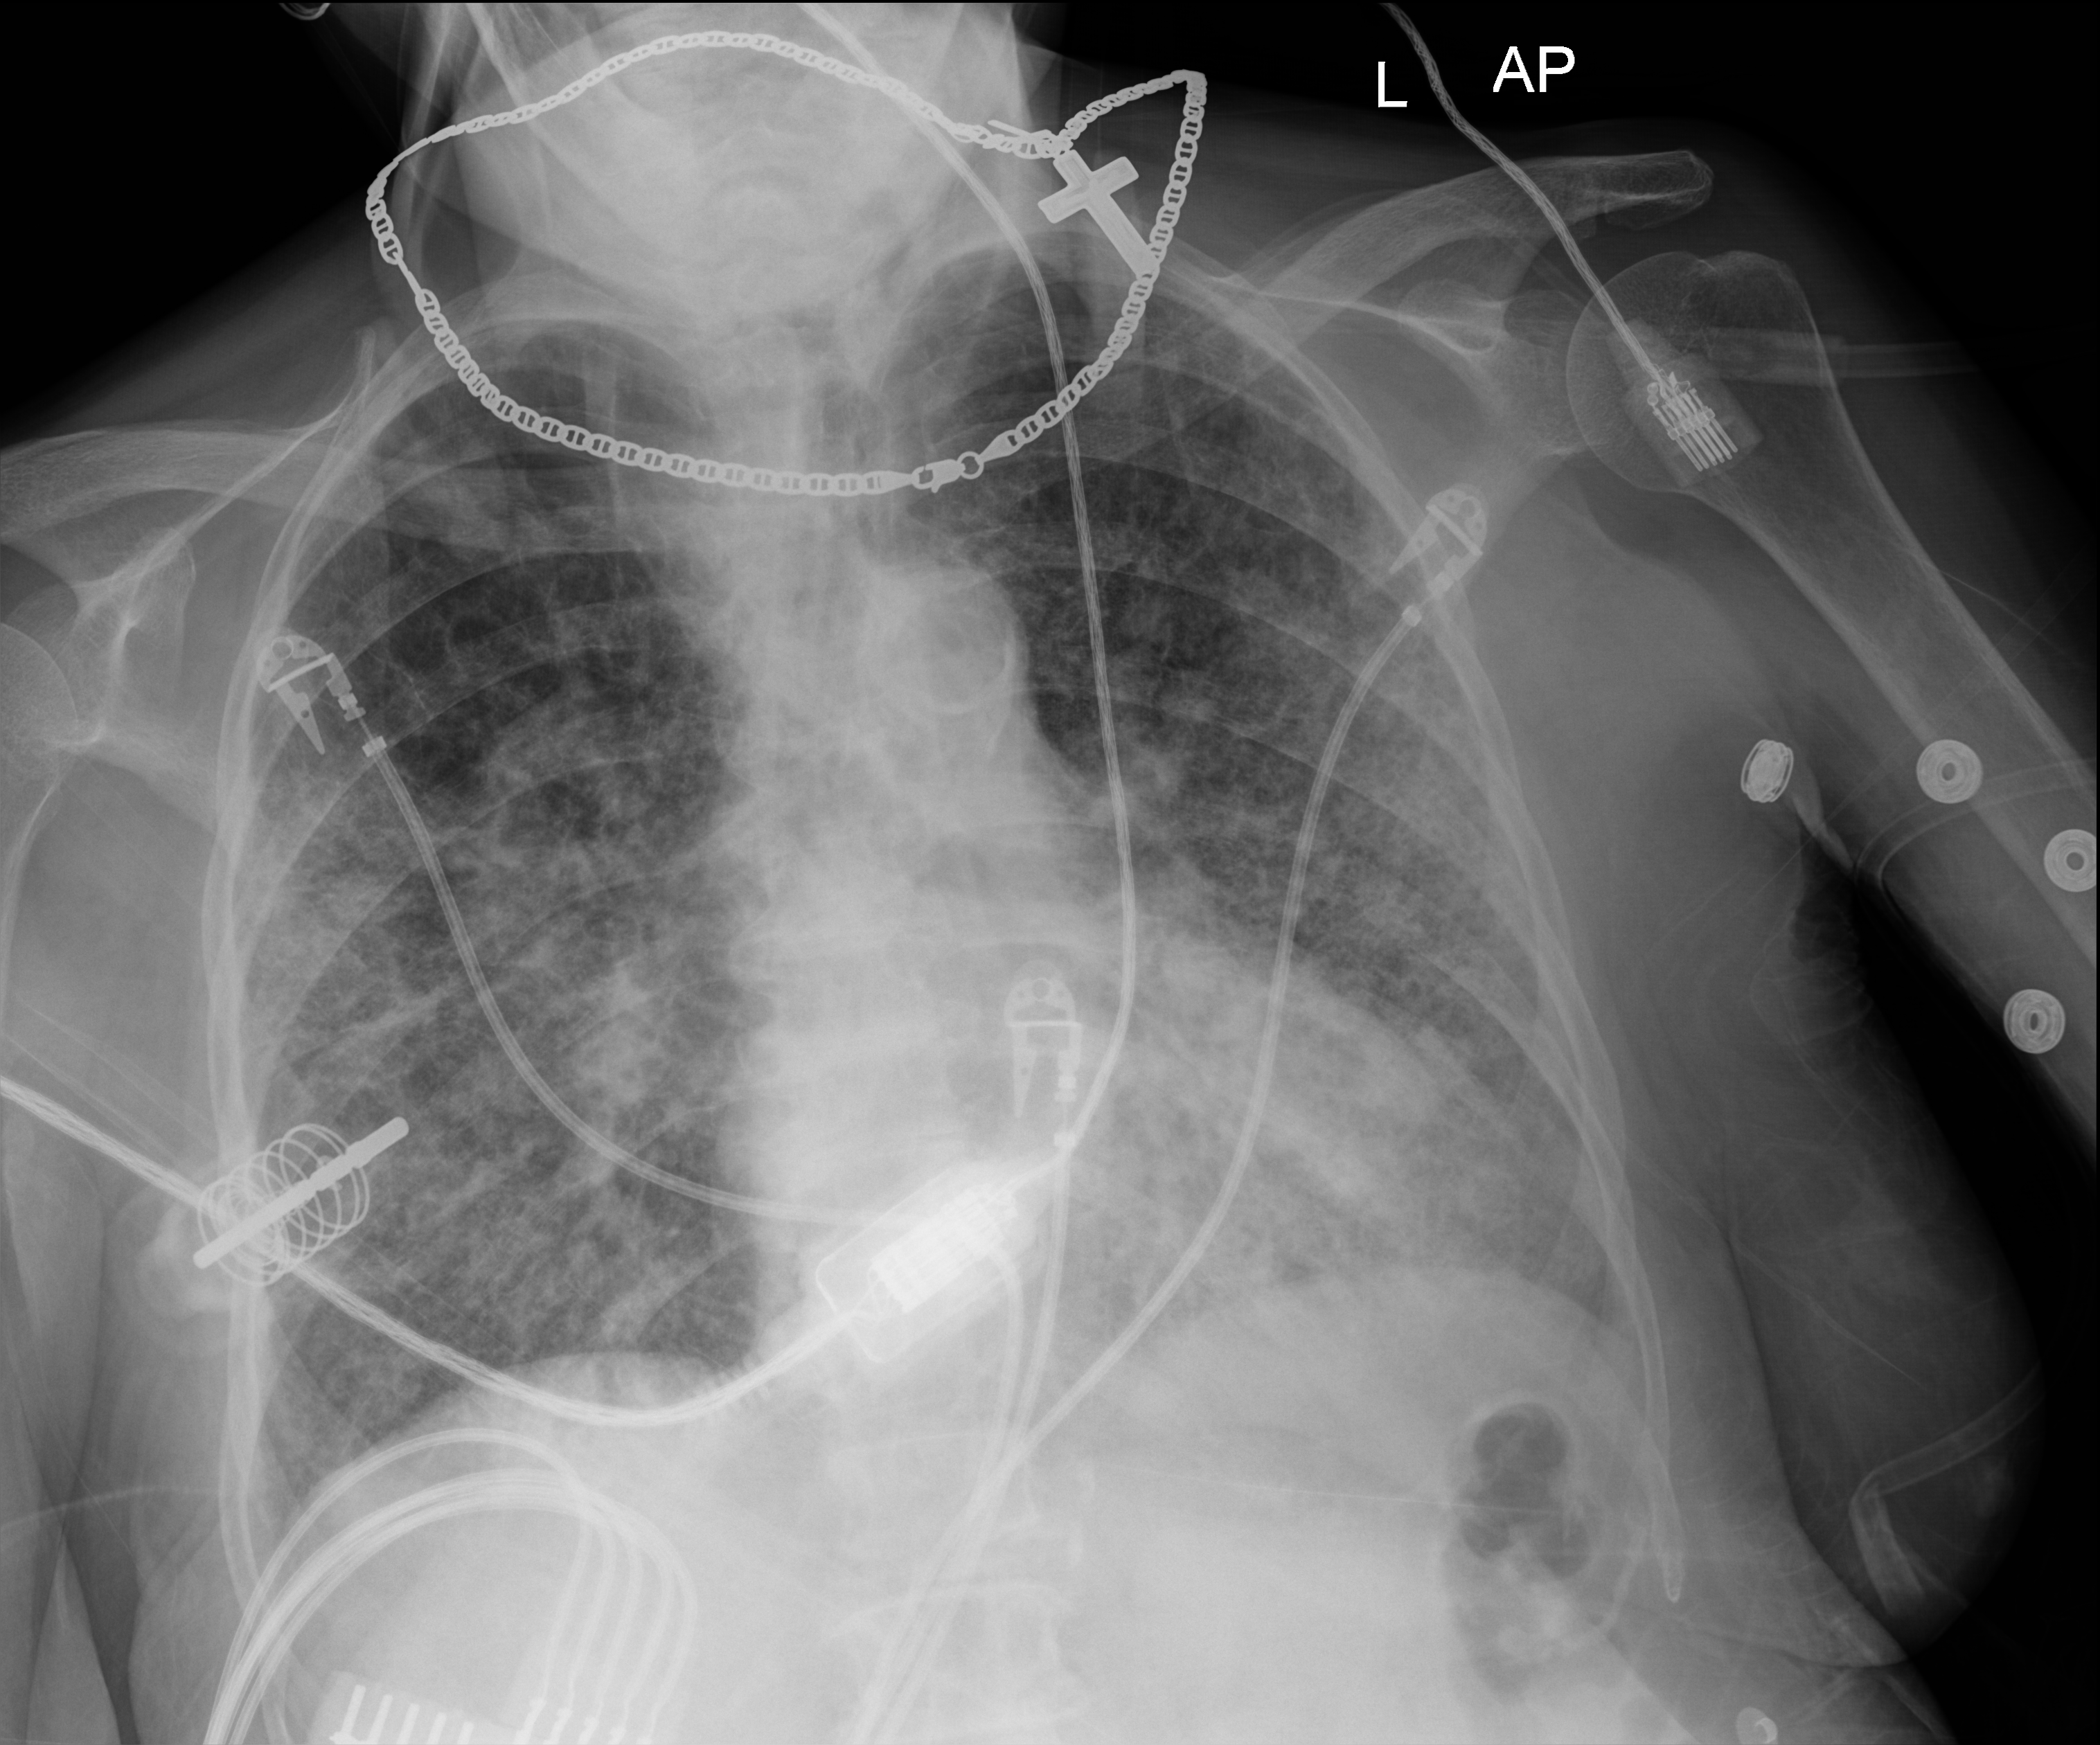
Chest X-ray (portable). Patient hospitalised with COVID-19; female, aged 75–90 years.
Admission-level facts for this patient (not findings on this image; timing relative to this image not recorded): admitted to intensive care during this hospital stay: no.